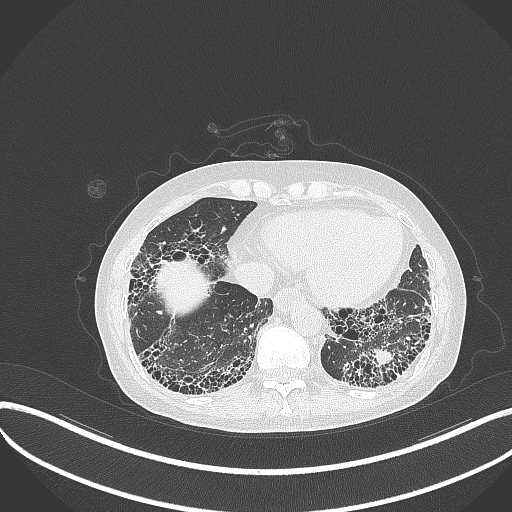
Chest CT, one axial slice; slice 74 of 373 in the series (ordered by position); reconstruction kernel B70f; 120 kVp; lung window (W 1500 / L -600 HU); 1 mm slice thickness; 512 × 512 image matrix, field of view 400 × 400 mm. Female patient, age 56 years. Case-level facts recorded for this patient, not image findings: clinical TNM (as recorded): T1 N0 M0.
Annotated regions visible in this slice (bounding box drawn by a radiologist):
- lung tumour (recorded histology: adenocarcinoma): bounding box <366,343,391,370> (left, top, right, bottom; pixels)